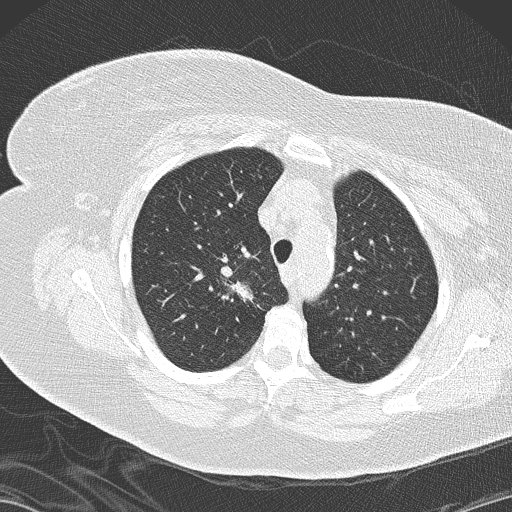
Chest CT (low-dose screening protocol), one axial image; second screening round (one year after baseline); lung window (W 1500 / L -600 HU); 120 kVp; slice 35 of 146 in the series. Female participant, aged 72 years at enrolment. Former smoker at enrolment.
• Expert reader's lesion annotation, bounding box <178,240,265,329> (left, top, right, bottom; pixels).
• The screening reader recorded 4 non-calcified nodules or masses ≥4 mm on this exam (right lower lobe, right lower lobe, right lower lobe, right upper lobe); which of them this box marks is not recorded.